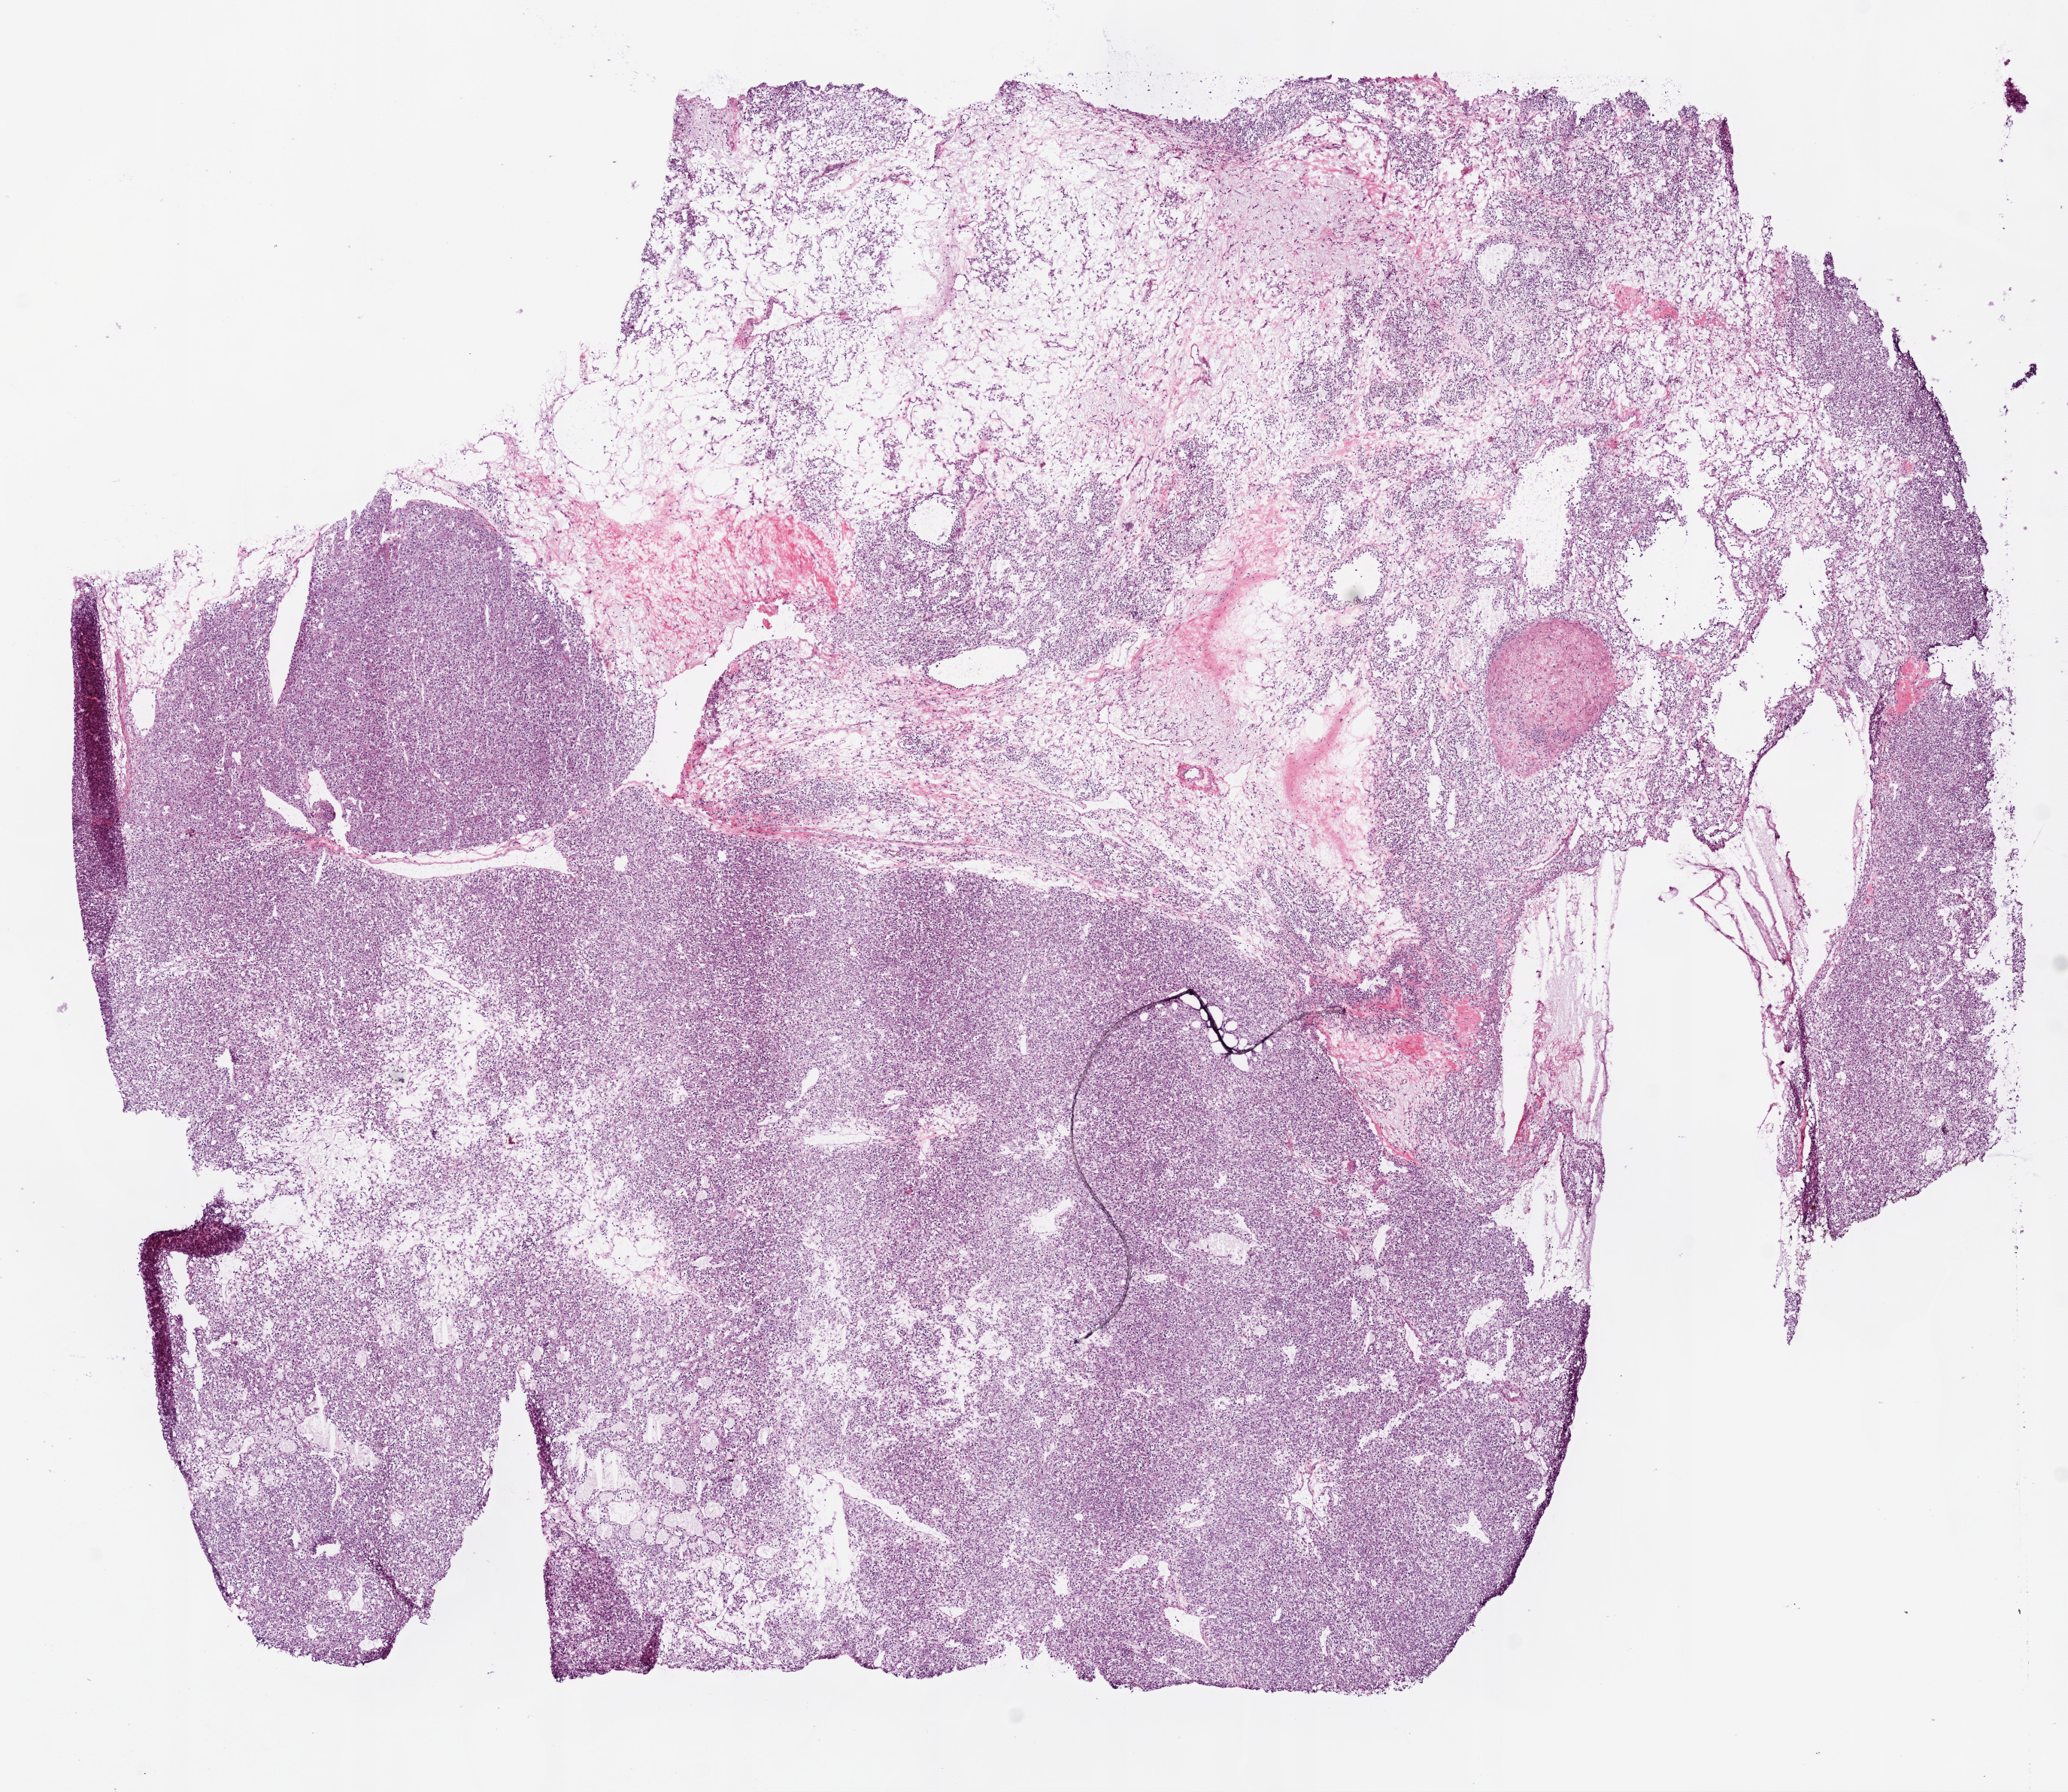
Digitized Hematoxylin and eosin (H&E) stained tissue section (whole slide), low-resolution overview of the scanned area, about 11.0 x 9.6 mm (slide scanned at 20x), frozen section, sample: primary tumour, kidney. Male, age 83 years at initial diagnosis. Histologic grade: G3 (poorly differentiated). Composition of this section per pathologist review: tumour cells 100%, tumour nuclei 99%, normal cells 0%, stromal cells 0%, necrosis 0%. Infiltration values recorded for this section: lymphocyte infiltration 1%.
Pathologic diagnosis: Clear cell adenocarcinoma, NOS. AJCC pathologic stage: I (7th edition).